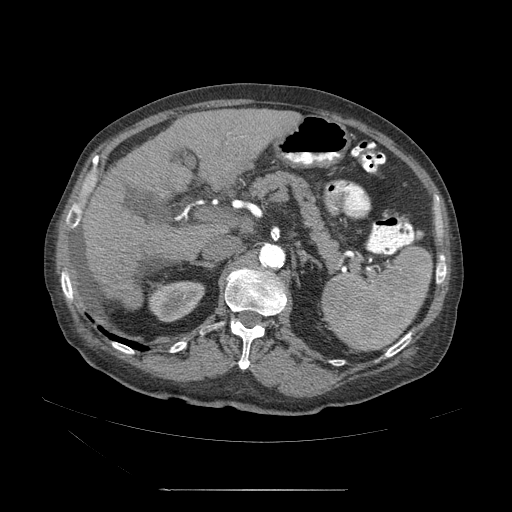
Contrast-enhanced abdominal CT (liver protocol), one axial slice. Slice 23 of 71 in the series (ordered by position). Reconstruction kernel STANDARD. 120 kVp. Soft-tissue window (W 400 / L 40 HU). 2.5 mm slice thickness. 512 × 512 image matrix. Case-level facts recorded for this patient, not image findings: diagnosis: hepatocellular carcinoma (patient treated with transarterial chemoembolisation; whether this scan precedes or follows treatment is not stated here); TNM stage (as recorded): Stage-II; Child-Pugh class: A; tumour nodularity: multinodular.
Outlined on this slice (semi-automatically segmented with operator editing):
- abdominal aorta: bounding box (x1, y1, x2, y2) in pixels: (261, 244, 286, 271)
- liver parenchyma outside the tumour (the mass and vessels are separate outlines, so this box may not span the whole liver): (83, 111, 288, 306)
- liver vessels: (184, 156, 242, 264)